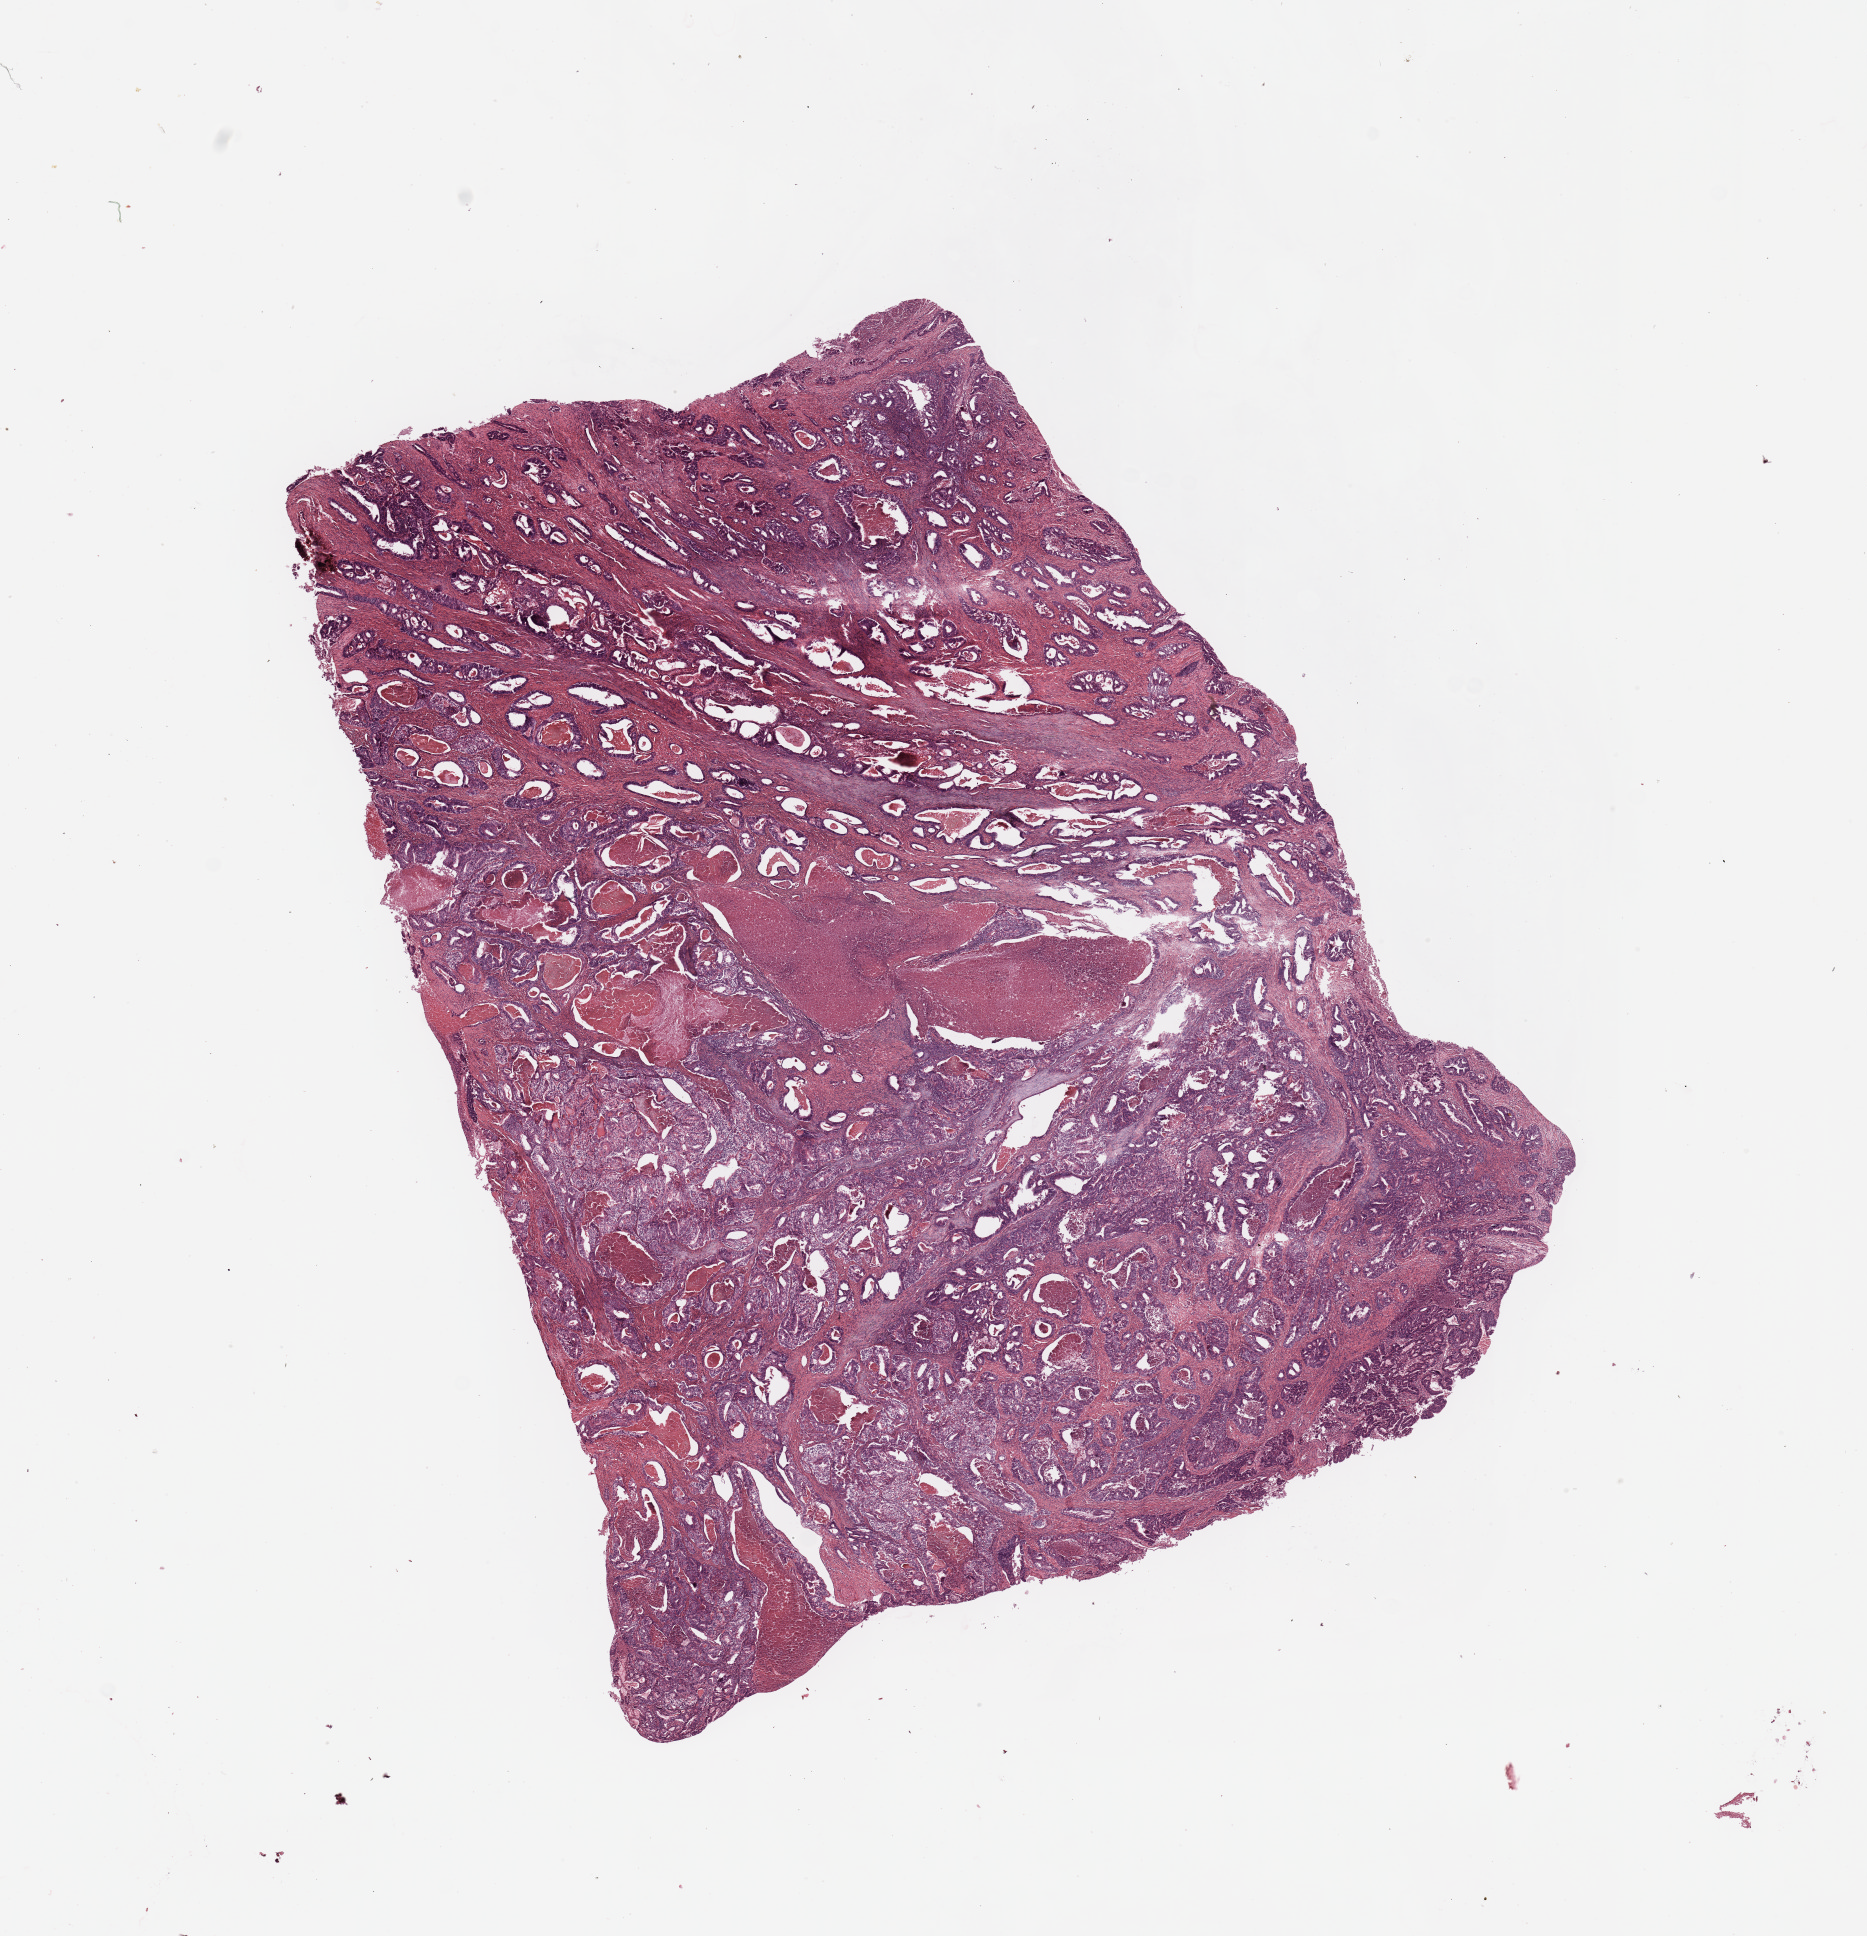
Hematoxylin and eosin (H&E) stained whole-slide image, a low-resolution overview of the entire scanned area, about 14.8 x 15.3 mm (from a 20x scan), tumour tissue sample, uterus. 68-year-old female patient. Histologic grade: G2 (moderately differentiated).
Histologic diagnosis: Endometrioid adenocarcinoma, NOS. AJCC pathologic stage: I.